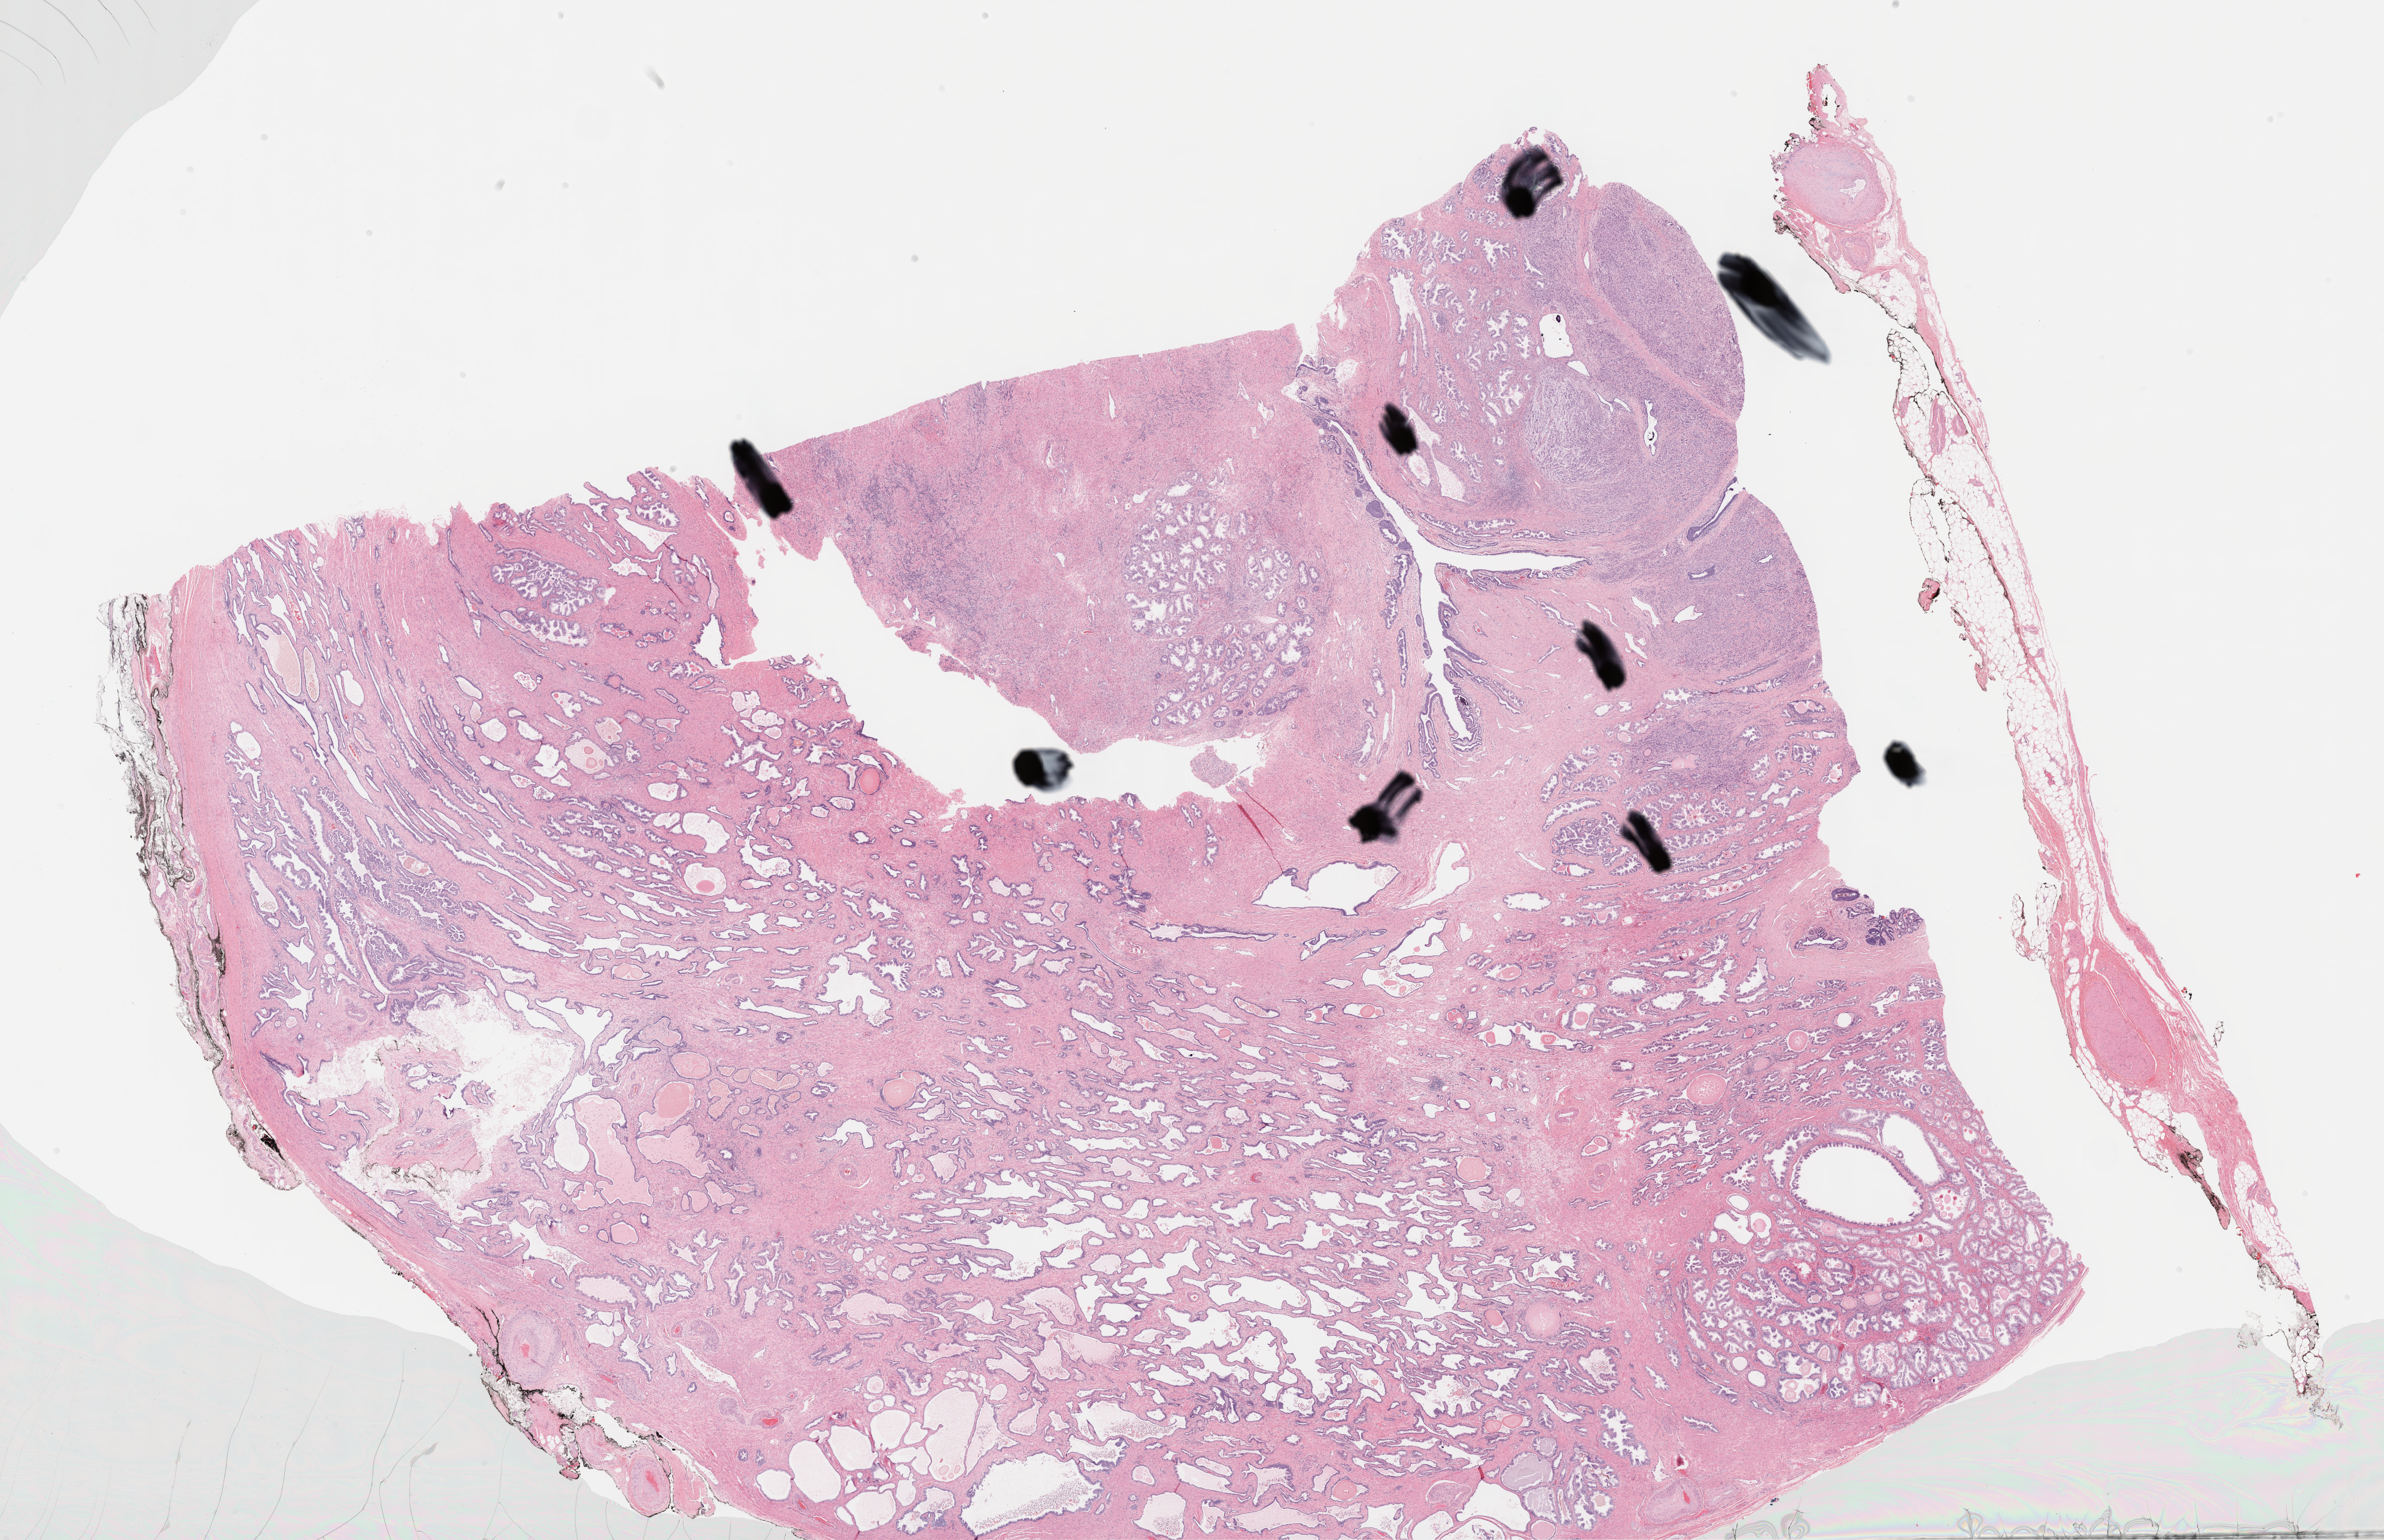
Digitized H&E-stained tissue section (whole slide), whole scanned area (about 32.2 x 20.8 mm) shown as a low-resolution overview, formalin-fixed paraffin-embedded (FFPE) diagnostic section, sample: primary tumour, prostate. Patient: male, age at initial diagnosis 64 years. Gleason score: 9 (4+5).
Lymph nodes positive (case pathology): 0 of 5 examined. Histologic diagnosis: Adenocarcinoma, NOS.